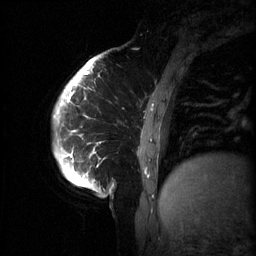
Breast MRI (dynamic contrast-enhanced), one sagittal slice; slice 9 of 60 in the series (ordered by position); 3 images stored at this slice position (order not interpretable as contrast timing); 1.5 T; TE 4.2 ms, TR 11 ms; 2 mm slice thickness; 256 × 256 image matrix, field of view 220 × 220 mm. Female patient, age 51 years.
Structures marked on this image (semi-automatic segmentation, software-assisted and operator-edited):
- analysis volume of interest (the breast-tissue region the enhancement analysis was run in; not a lesion): bounding box <63,80,187,201> (left, top, right, bottom; pixels)
- tumour enhancement mask (voxels above the 70 % enhancement threshold inside the analysis volume of interest): <66,82,153,173>